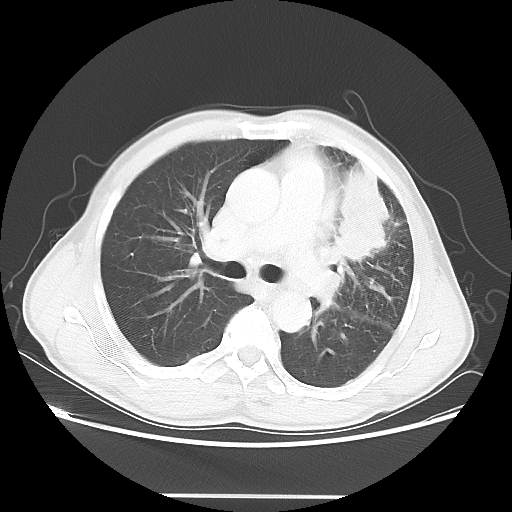
Chest CT, one axial slice. Slice 32 of 55 in the series (ordered by position). Reconstruction kernel LUNG. Lung window (W 1500 / L -600 HU). 512 × 512 image matrix, field of view 398 × 398 mm. Patient: male, 60 years. Case-level facts recorded for this patient, not image findings: clinical TNM (as recorded): T3 N3 M0.
Structures marked on this image (rectangle marked by the reading radiologist):
- lung tumour (recorded histology: adenocarcinoma): bounding box [x1, y1, x2, y2] px = [334, 150, 395, 268]